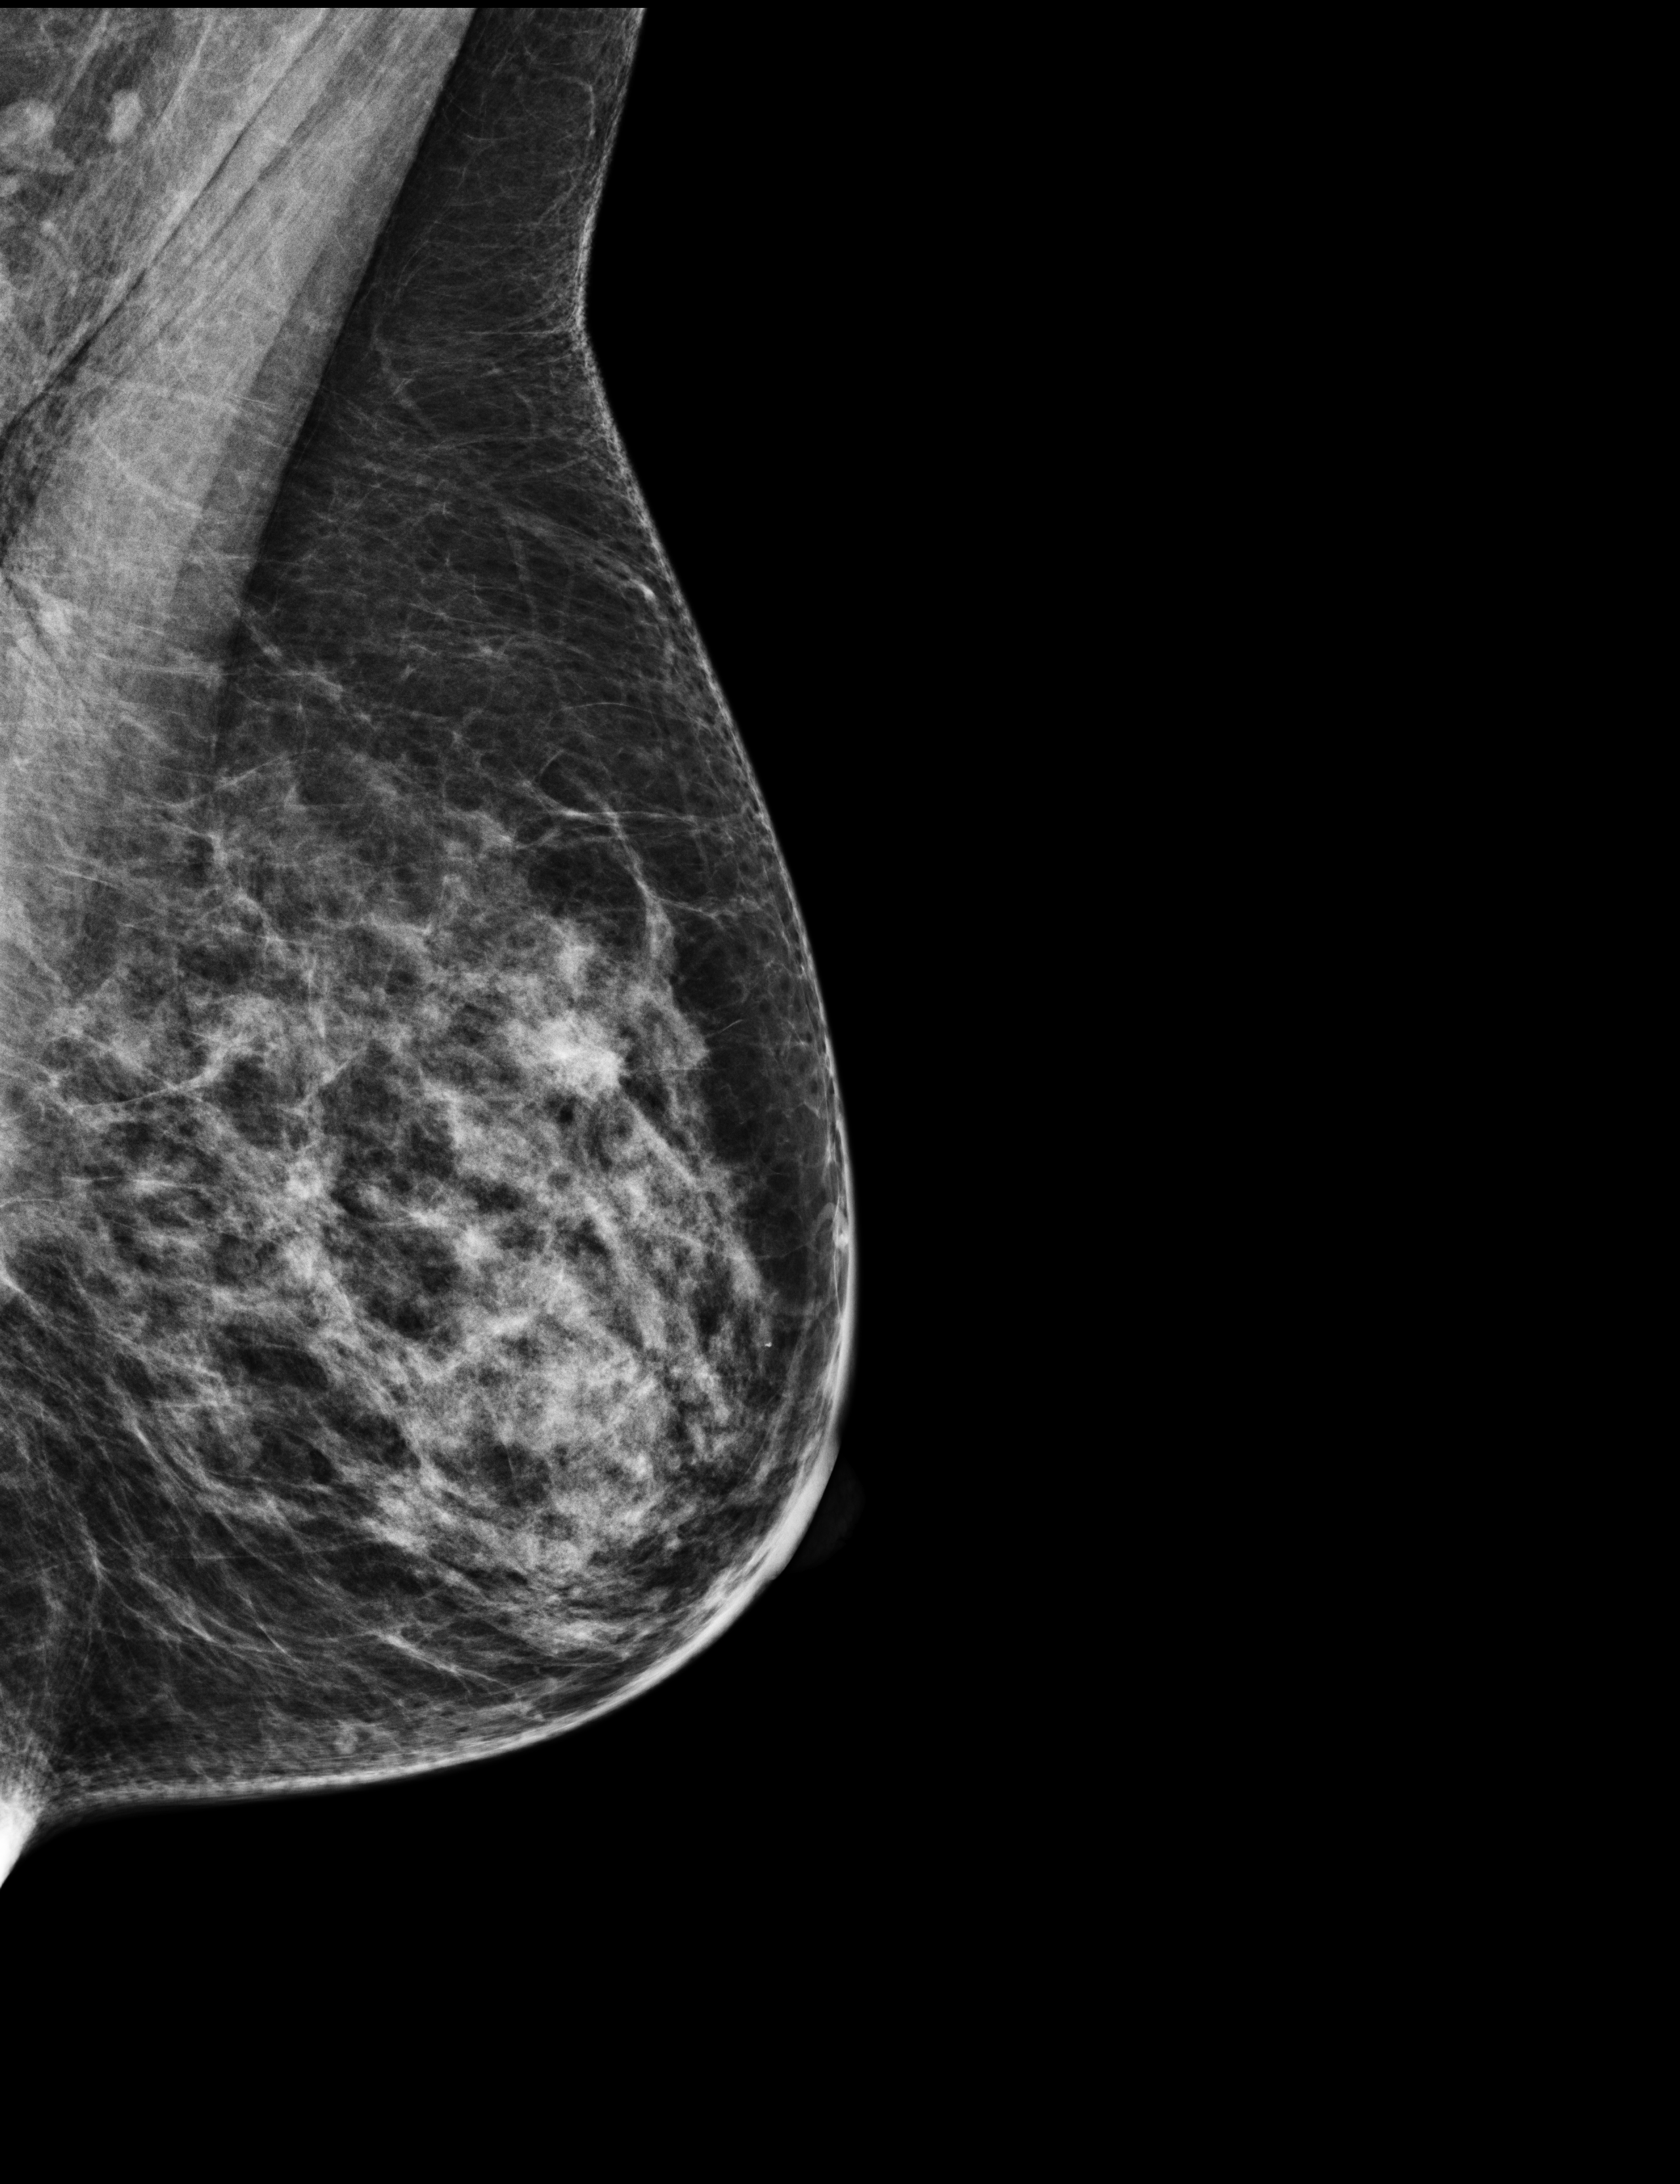
Screening examination, compressed breast thickness 56 mm, system: Selenia Dimensions. Patient aged 61 years (female).
Image type: full-field digital mammogram. Breast: left. Projection: MLO view.